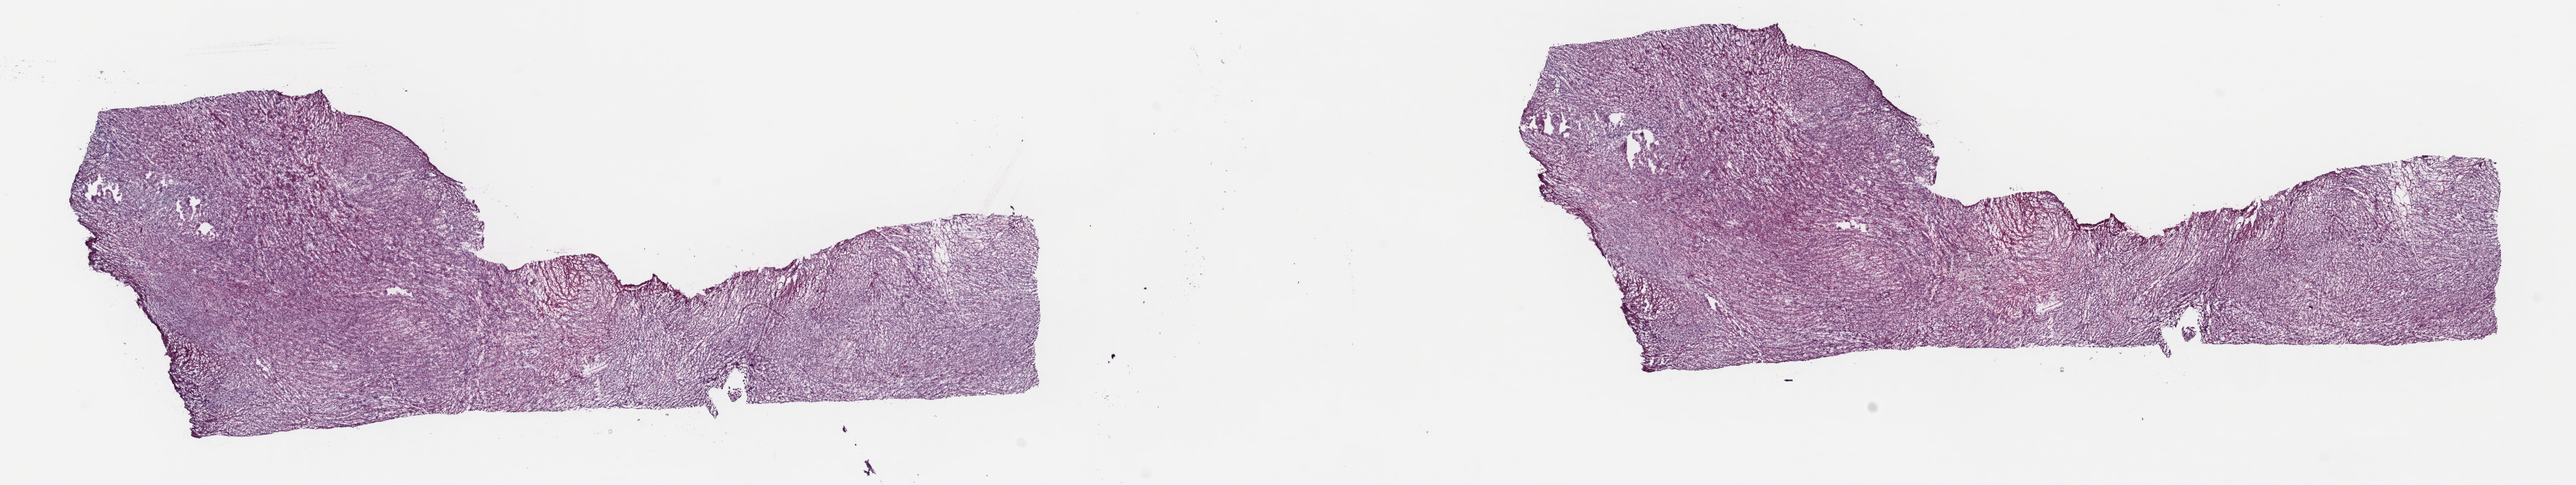
H&E-stained whole-slide image — whole scanned area (about 29.7 x 5.6 mm, slide scanned at 40x) shown as a low-resolution overview, frozen section from the top of the tissue portion, retroperitoneum and peritoneum, primary tumour sample. Patient: female, age at initial diagnosis 82 years. Pathologist review of this section (percent, as recorded): tumour cells 100%, tumour nuclei 80%, normal cells 0%, stromal cells 0%, necrosis 0%. Inflammatory infiltration, as recorded: lymphocyte infiltration 1%, monocyte infiltration 0%, neutrophil infiltration 0%.
• pathologic diagnosis: Dedifferentiated liposarcoma (retroperitoneum)